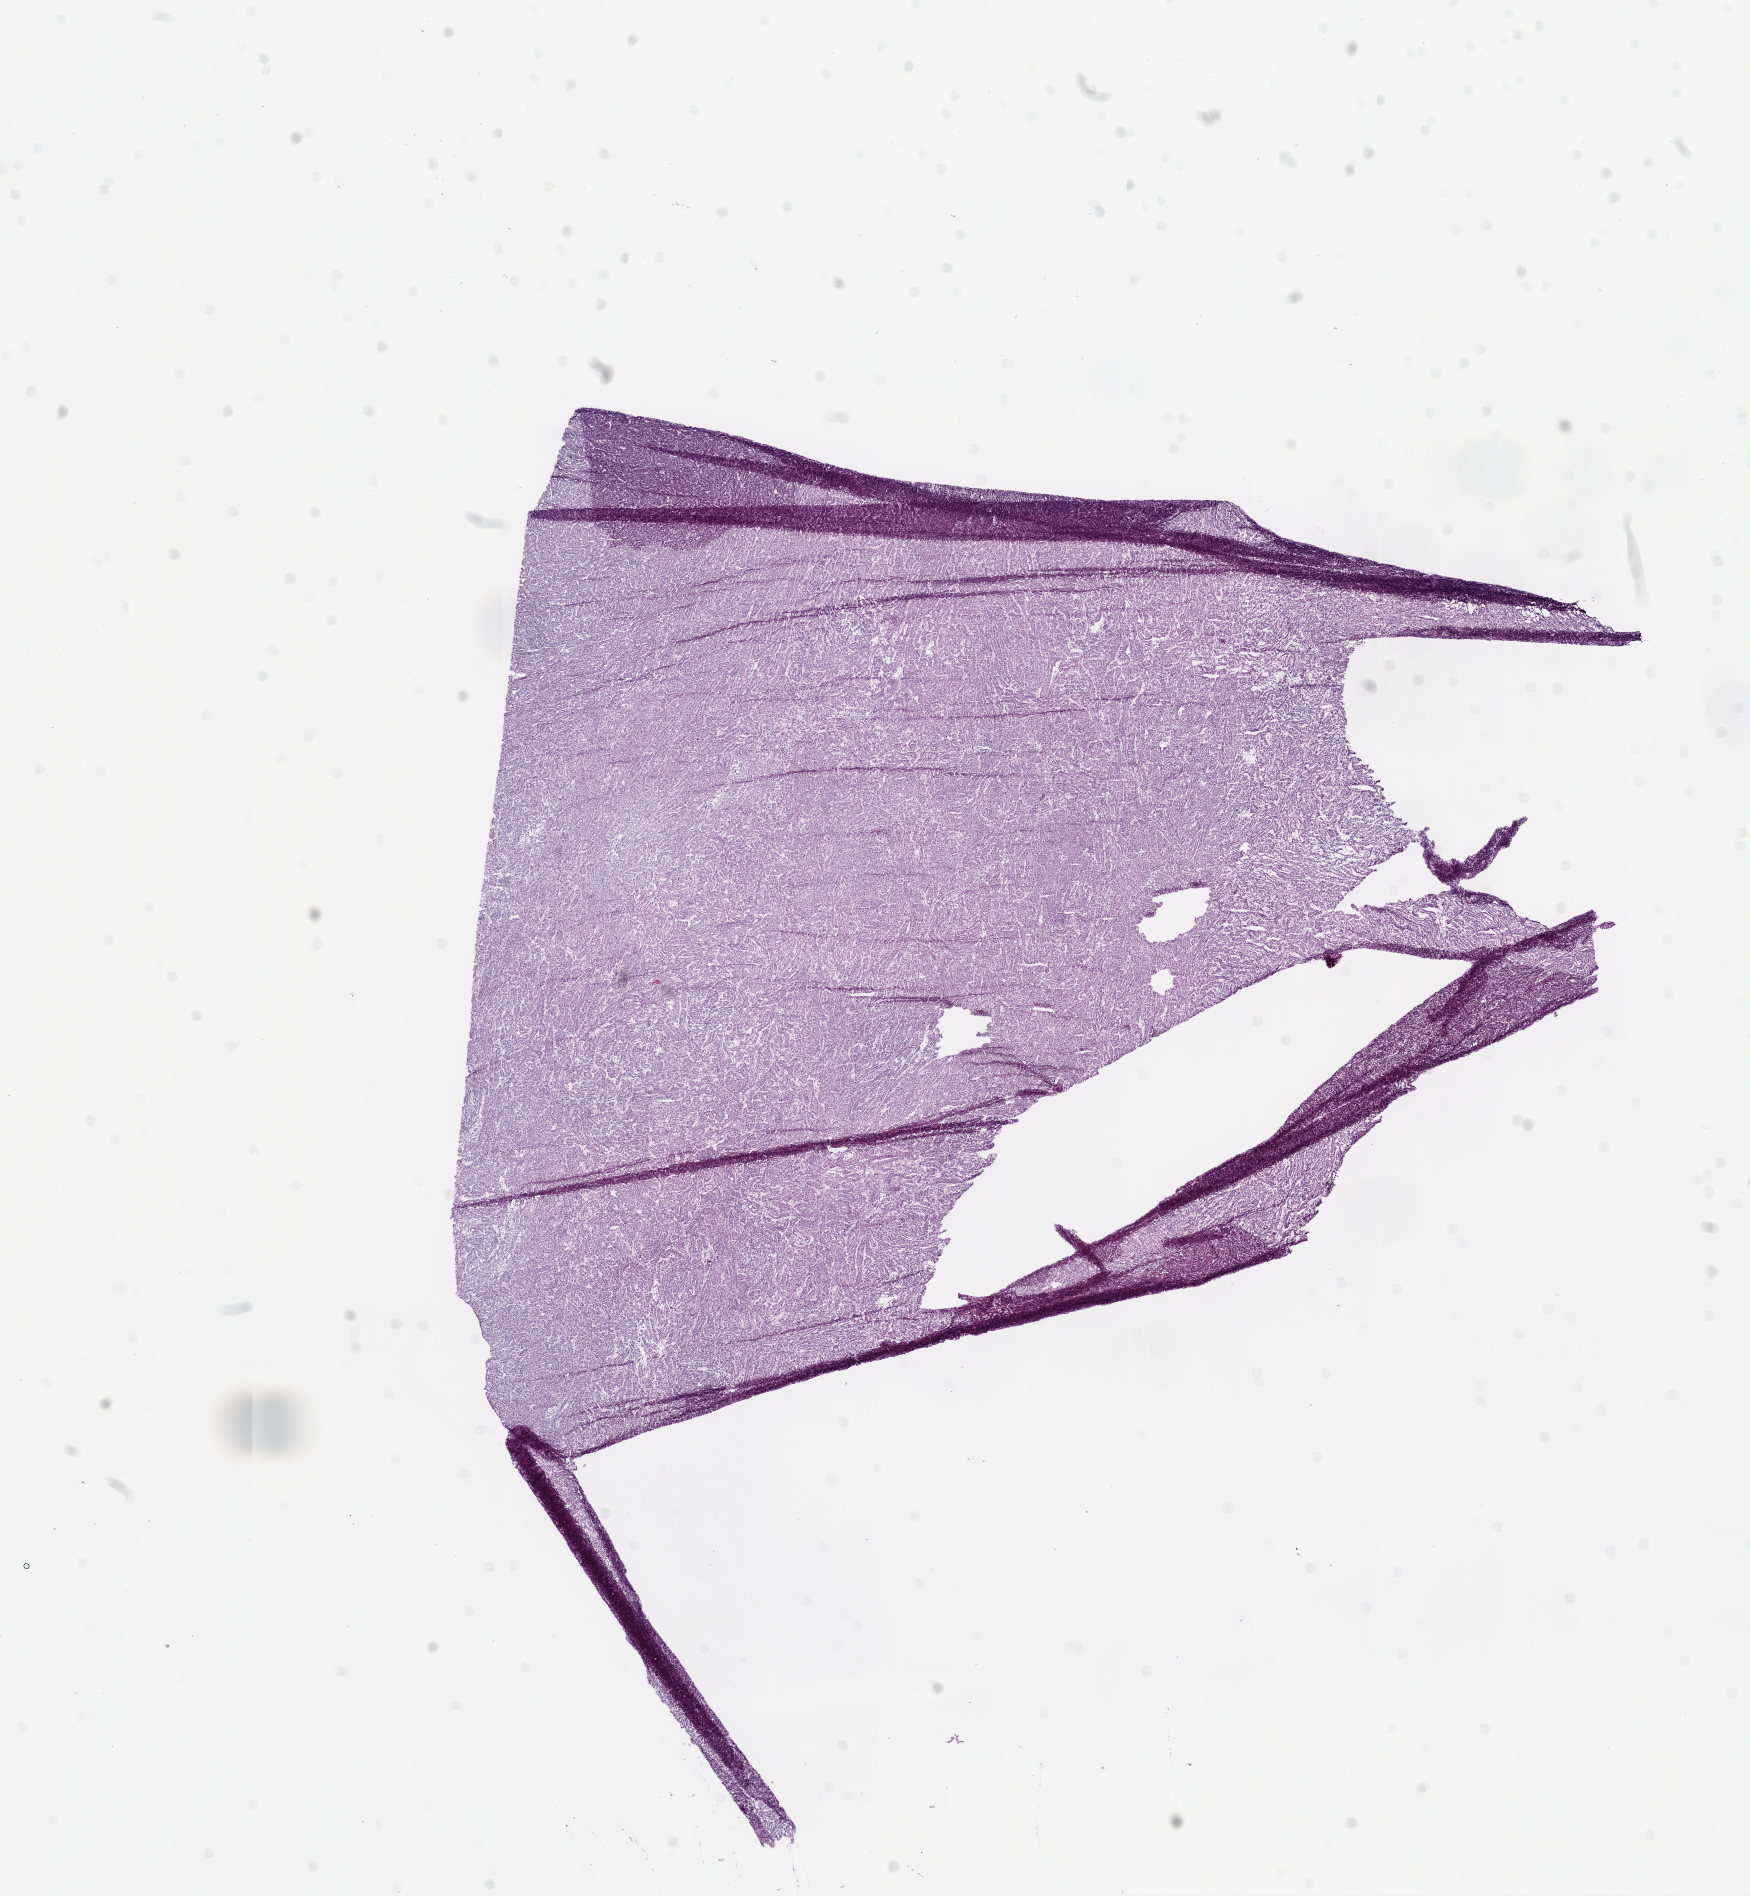
Whole-slide histology image, Hematoxylin and eosin (H&E) stained, whole scanned area (about 14.0 x 15.2 mm, slide scanned at 20x) shown as a low-resolution overview. Frozen section from the bottom of the tissue portion. Primary tumour sample from the kidney. Patient: female, age at initial diagnosis 59 years. Composition of this section per pathologist review: tumour cells 98%, tumour nuclei 90%, normal cells 0%, stromal cells 2%, necrosis 0%.
* AJCC pathologic stage: I
* diagnosis: Papillary adenocarcinoma, NOS